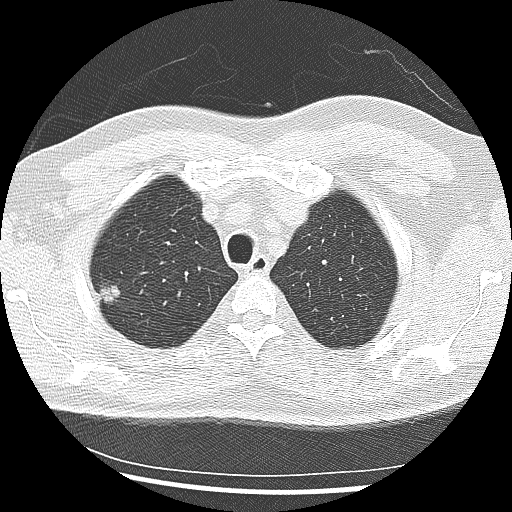
Low-dose screening chest CT, one axial slice; slice 218 of 265 in the series (ordered by position); 120 kVp; lung window (W 1500 / L -600 HU); 2.5 mm slice thickness; 512 × 512 image matrix.
Annotated regions visible in this slice (expert manual segmentation):
- lesion 1 (tumor, upper lobe of right lung): bounding box [x1, y1, x2, y2] px = [100, 285, 120, 302]